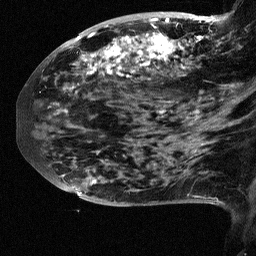
Breast MRI (dynamic contrast-enhanced), one sagittal slice; slice 26 of 64 in the series (ordered by position); dynamic contrast-enhanced study with each time point stored as its own series, time point 2 of 3 at this slice position (early post-contrast, ordered by acquisition time); 1.5 T; TE 4.5 ms, TR 11 ms; 2.5 mm slice thickness; 256 × 256 image matrix, field of view 200 × 200 mm. Female patient, age 38 years. From the clinical record (not read from this slice): setting: breast cancer imaged before/during neoadjuvant chemotherapy; receptor status: HR-positive, HER2-negative.
Structures marked on this image (semi-automatic segmentation, software-assisted and operator-edited):
- analysis volume of interest (the breast-tissue region the enhancement analysis was run in; not a lesion): bounding box <88,18,252,126> (left, top, right, bottom; pixels)
- tumour enhancement mask (voxels above the 90 % enhancement threshold inside the analysis volume of interest): <88,18,228,113>